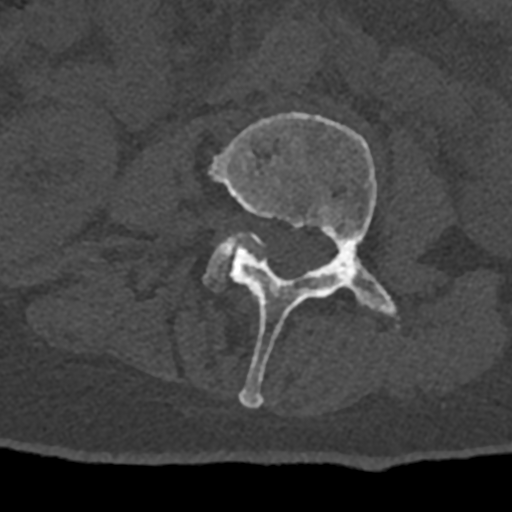
CT including the spine, one axial slice. Position 311 of 797 along the scan axis. Reconstruction kernel Br40s/3. 120 kVp. Bone window (W 1800 / L 400 HU). 0.5 mm slice thickness. 512 × 512 image matrix, field of view 160 × 160 mm. Patient: male, 74 years. Case-level facts recorded for this patient, not image findings: primary cancer: renal.
Annotated regions visible in this slice (semi-automatic segmentation, software-assisted and operator-edited):
- L3 vertebra: box from (x=210, y=112) to (x=399, y=408) px
- L4 vertebra: (x=207, y=233)–(x=265, y=290)